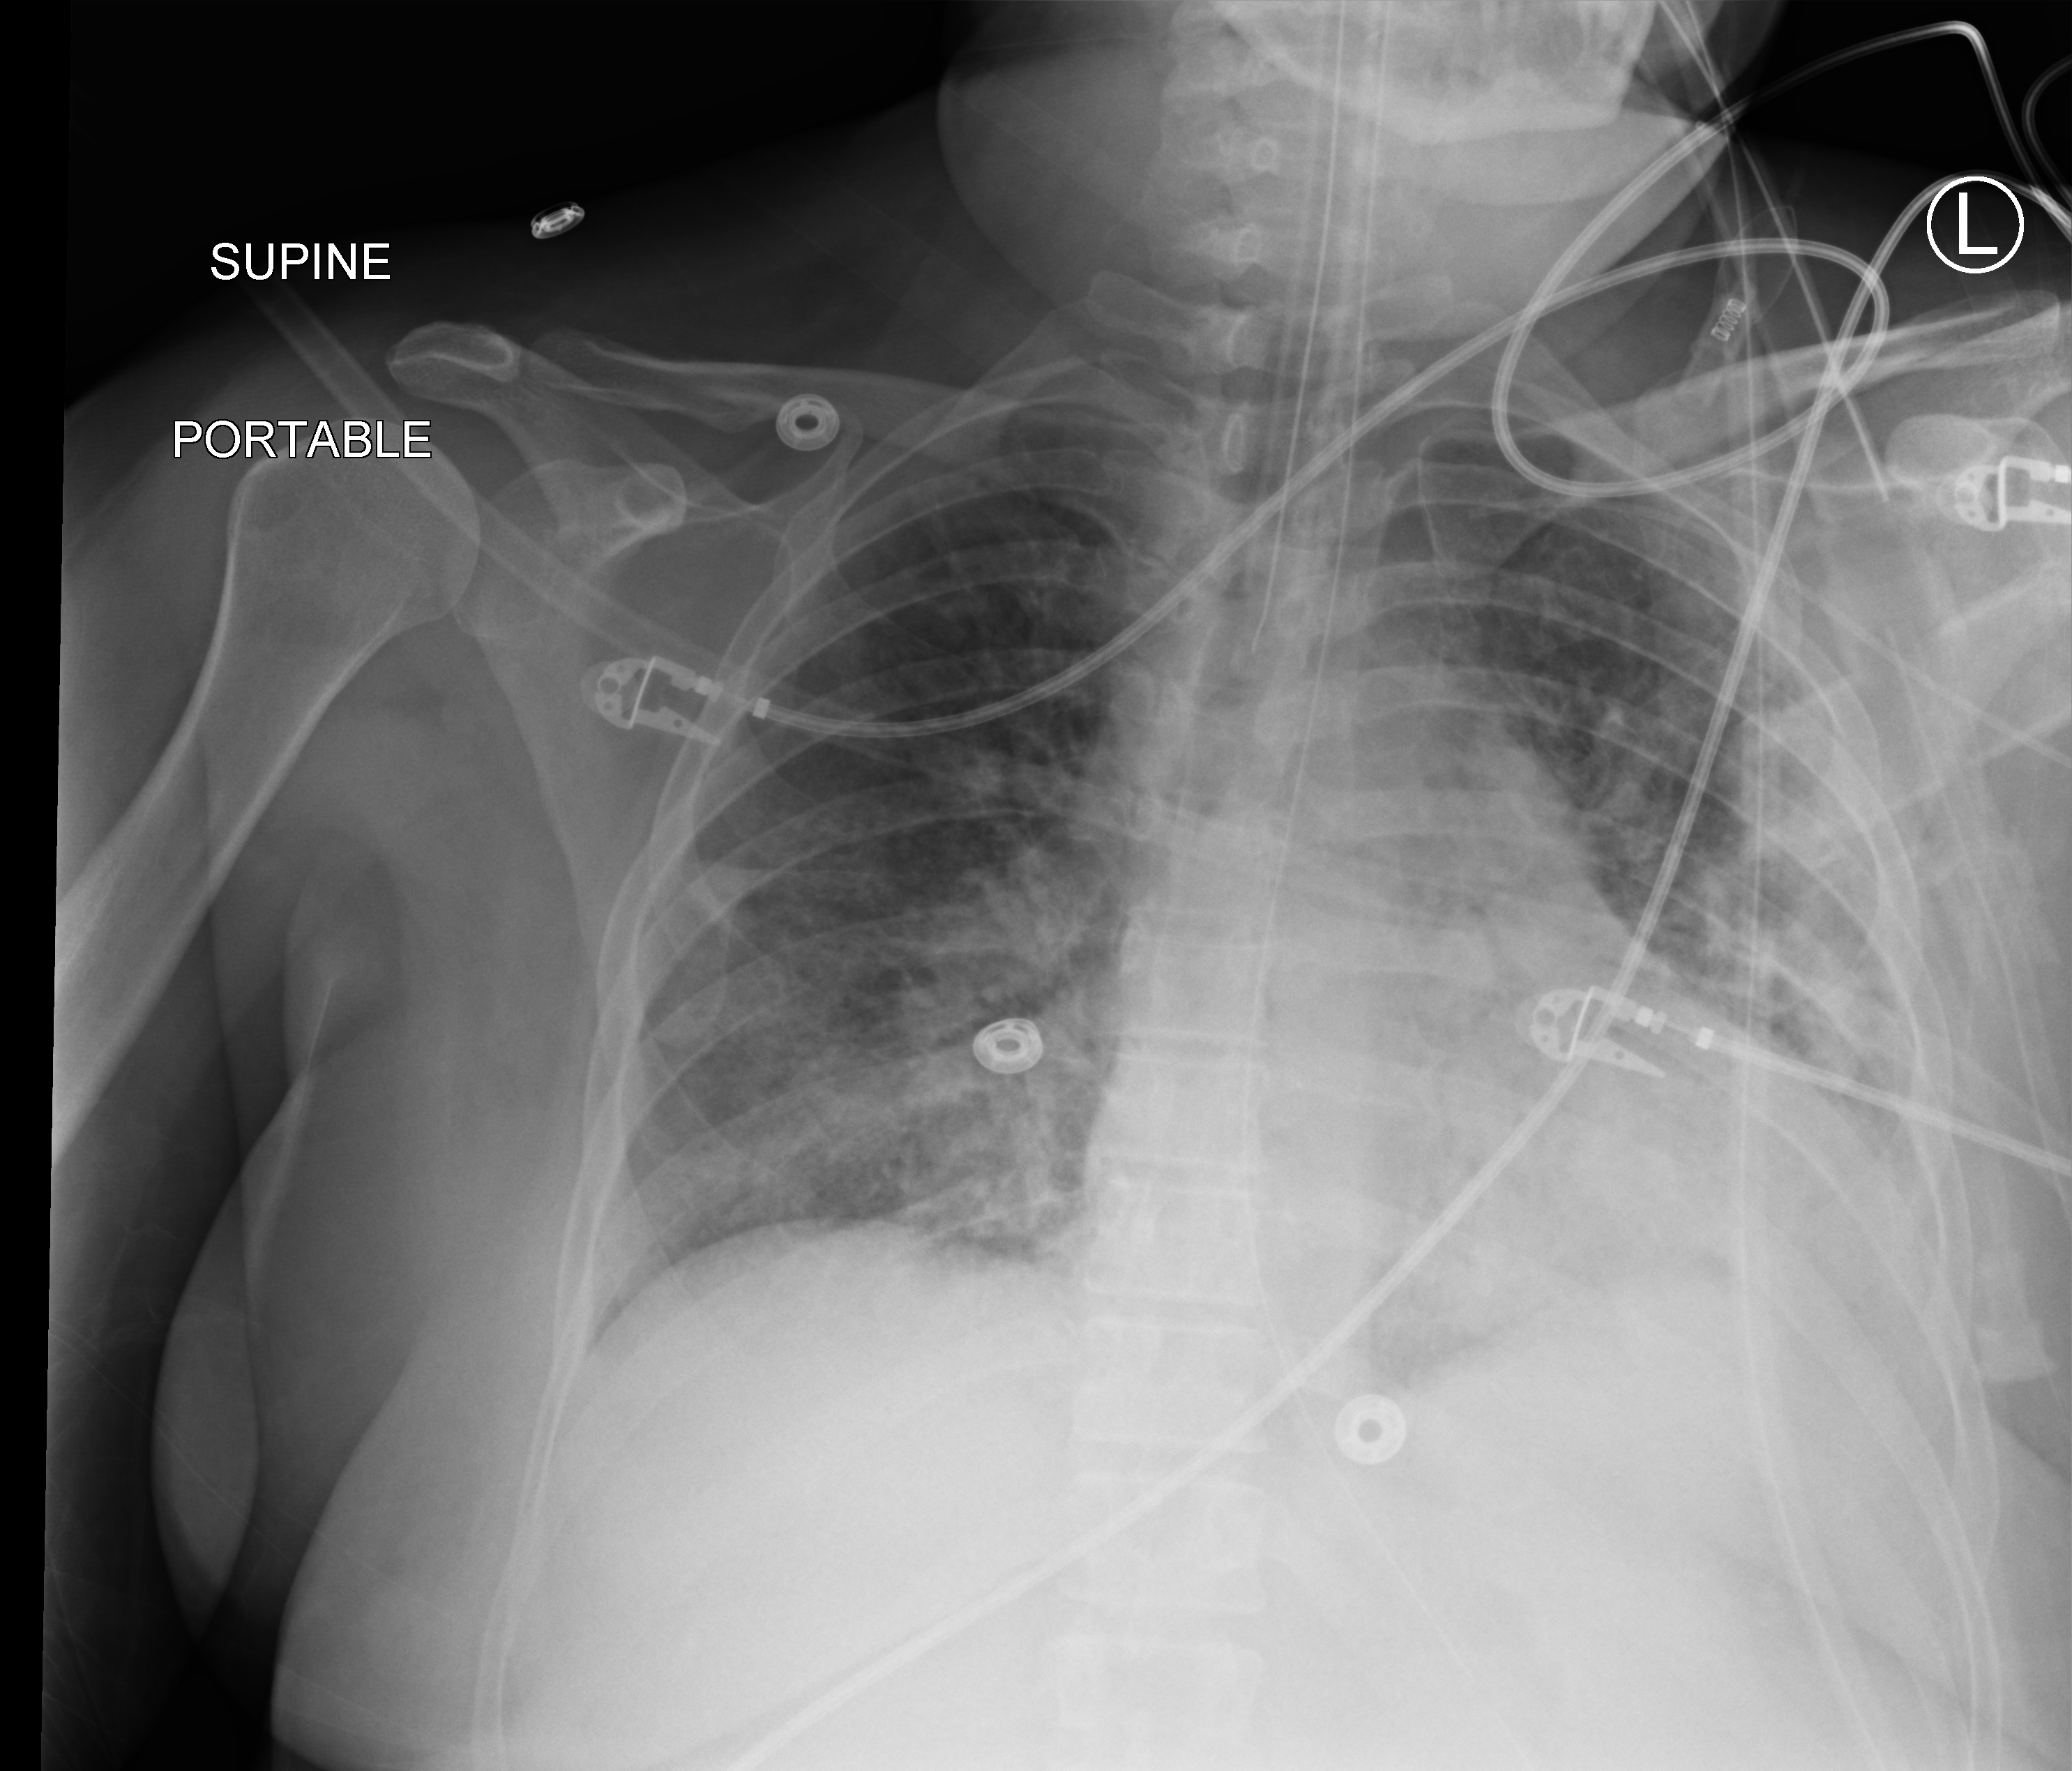
Chest X-ray (portable), anteroposterior (AP) projection. Patient hospitalised with COVID-19; female, aged 18–59 years.
Hospital-stay facts (about this admission, not read from this image; timing relative to this image not recorded): mechanically ventilated during this hospital stay: yes; diabetes (admission record): yes.